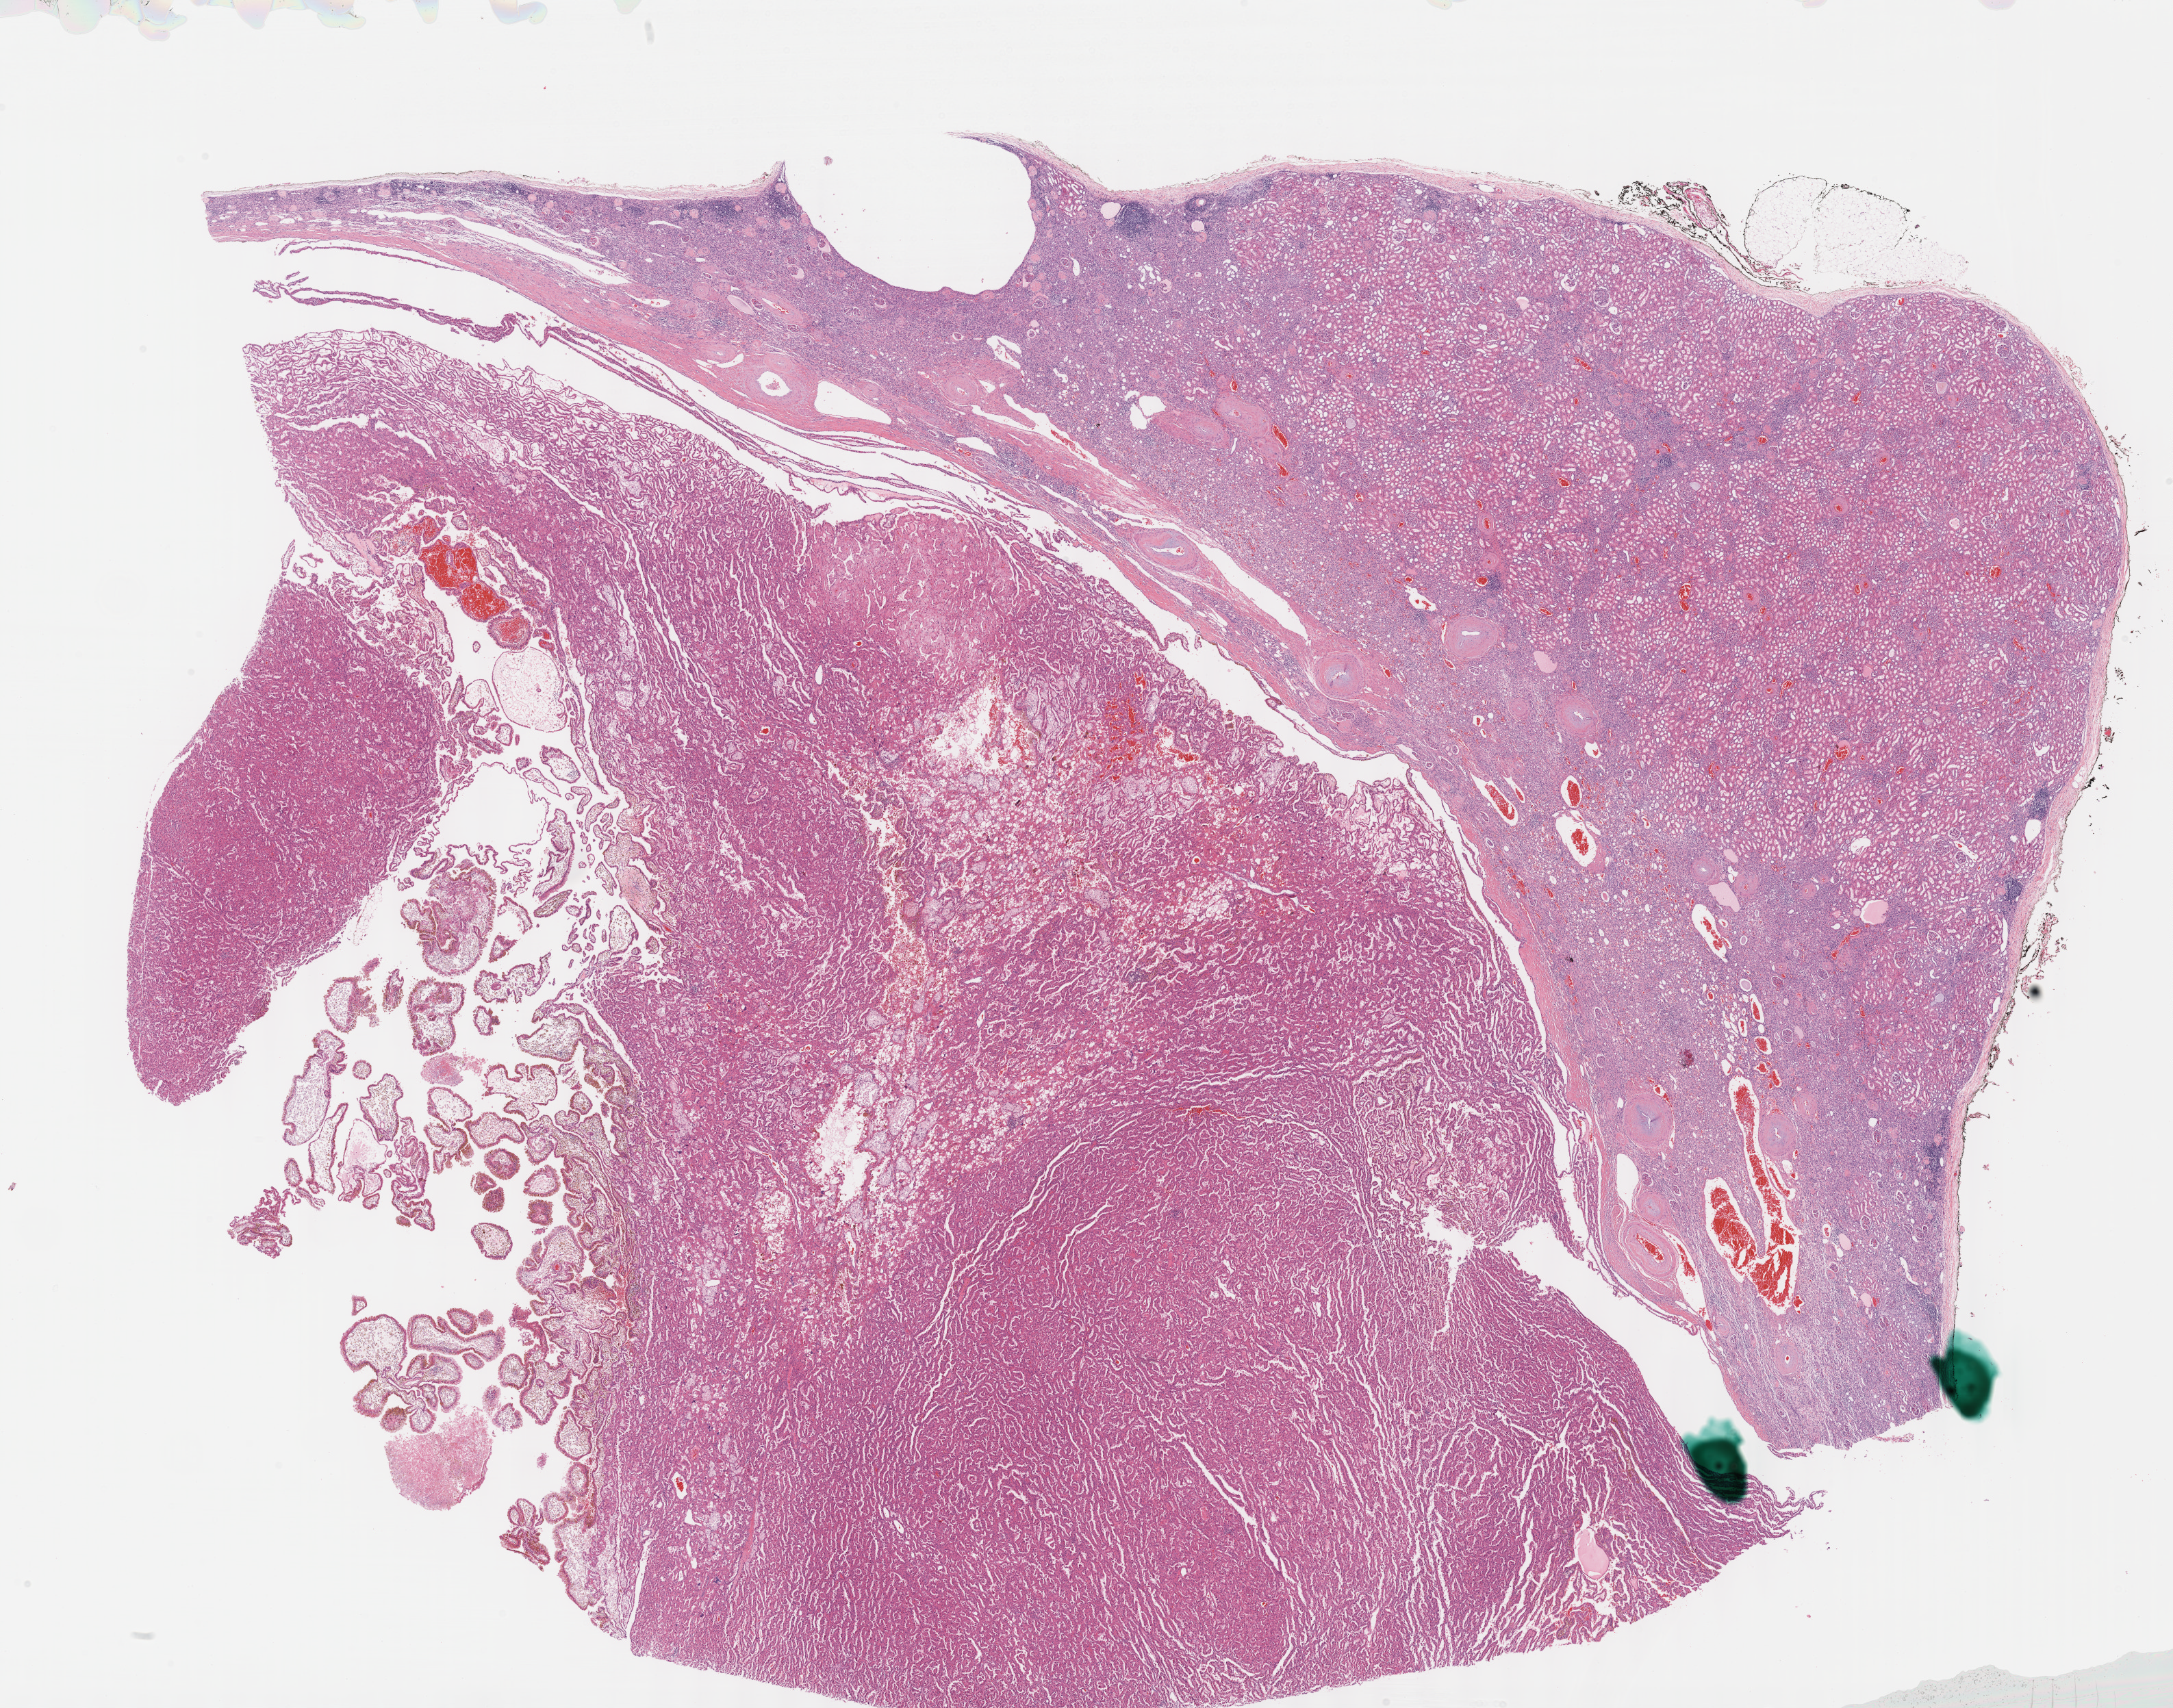
Hematoxylin and eosin (H&E) stained whole-slide image, shown as a low-resolution overview of the whole scanned area (about 25.7 x 20.2 mm, from a 40x scan); FFPE section; kidney, primary tumour sample. Patient sex: female.
AJCC pathologic stage: I (6th edition). Histologic diagnosis: Papillary adenocarcinoma, NOS.